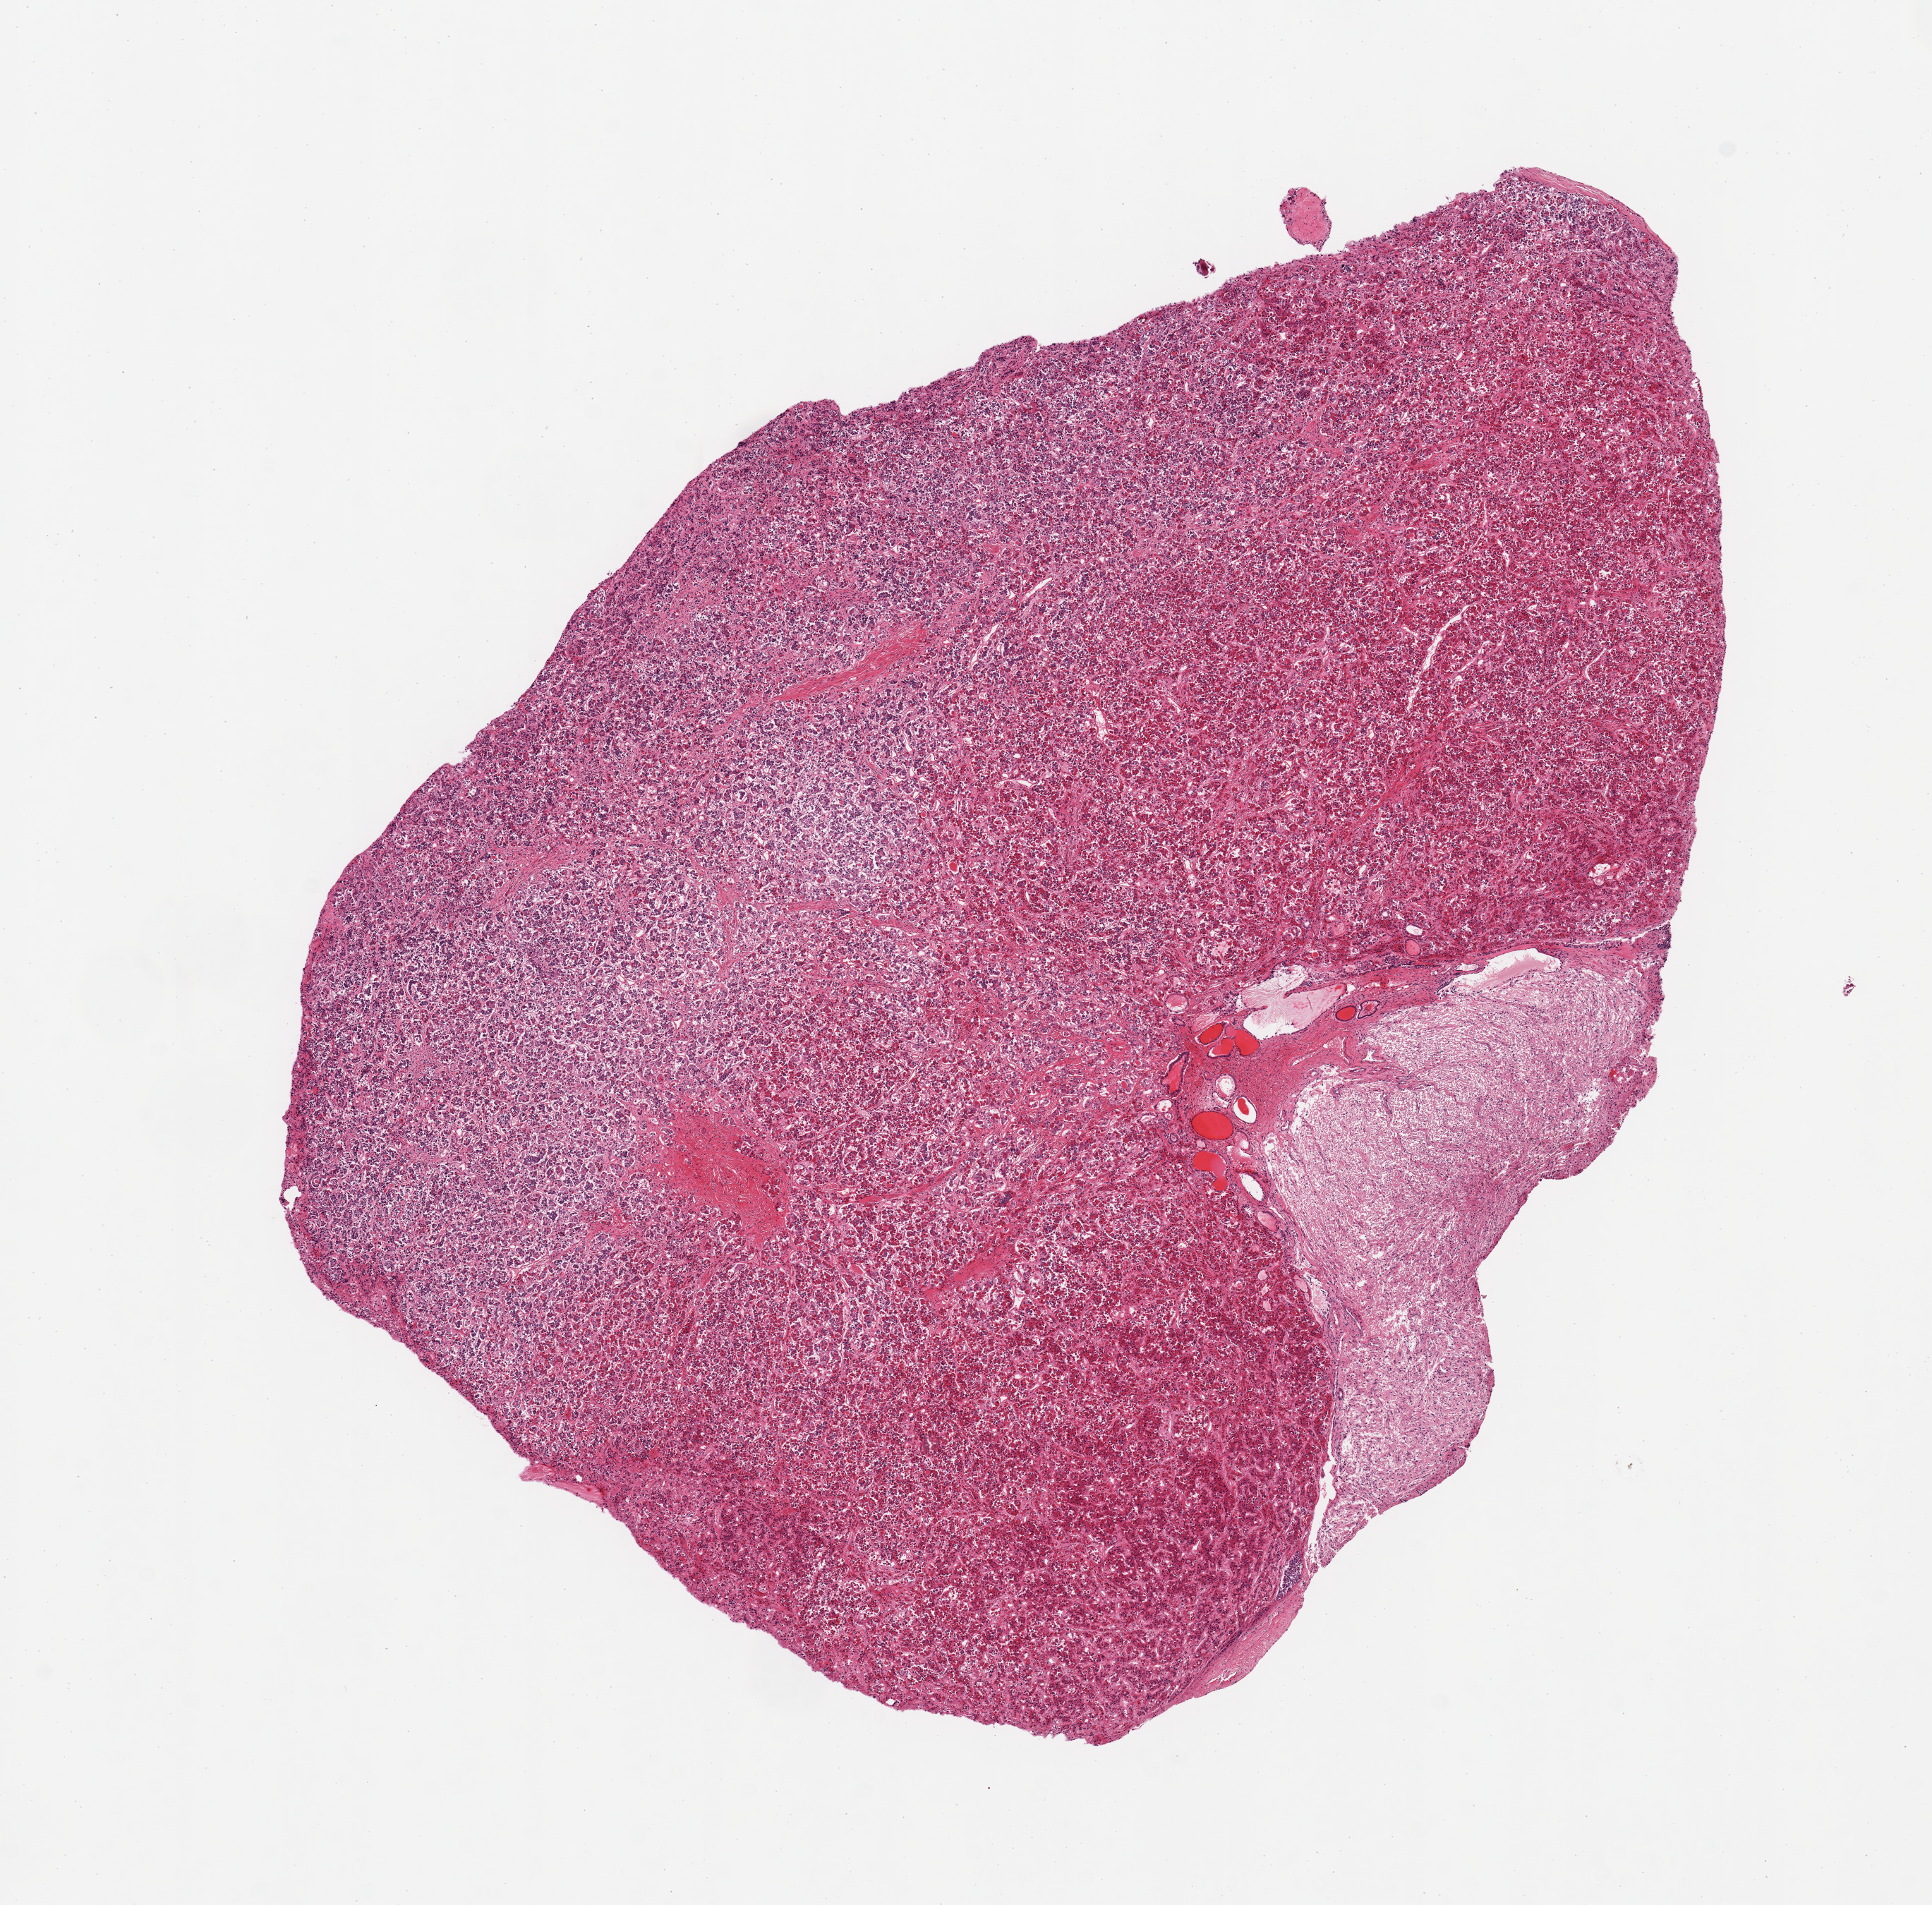
Haematoxylin and eosin whole-slide image, whole scanned area (about 10.8 x 10.7 mm, from a 20x scan) shown as a low-resolution overview. PAXgene-fixed paraffin-embedded (PFPE) section. Target tissue: pituitary. Tissue donor sample. Donor: male.
- review note (as recorded): 1 piece; 85% adenohypophysis and 15% neurohypophysis